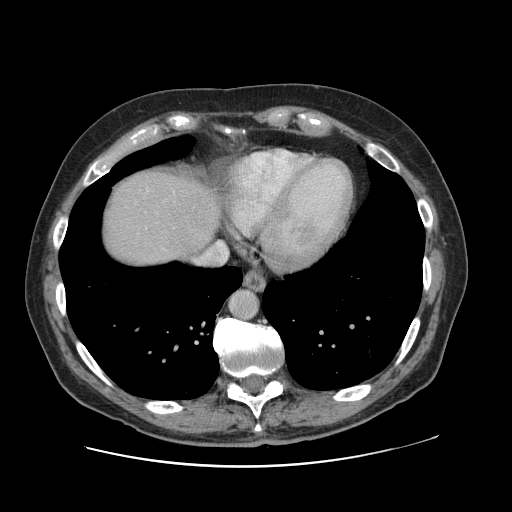
Contrast-enhanced abdominal CT, one axial slice; slice 110 of 138 in the series (ordered by position); intravenous contrast given; soft-tissue window (W 400 / L 40 HU); 2.5 mm slice thickness; 512 × 512 image matrix. Male patient, age 71 years. From the clinical record (not read from this slice): diagnosis: colorectal cancer liver metastases, imaged before liver resection; multiple liver metastases: no; largest metastasis: 3.3 cm; chemotherapy before resection: no.
Annotated regions visible in this slice (manually delineated by an expert):
- hepatic veins: box from (x=197, y=241) to (x=228, y=265) px
- liver: (x=101, y=168)–(x=220, y=268)
- planned liver remnant (the part of the liver to remain after resection): (x=101, y=170)–(x=215, y=268)